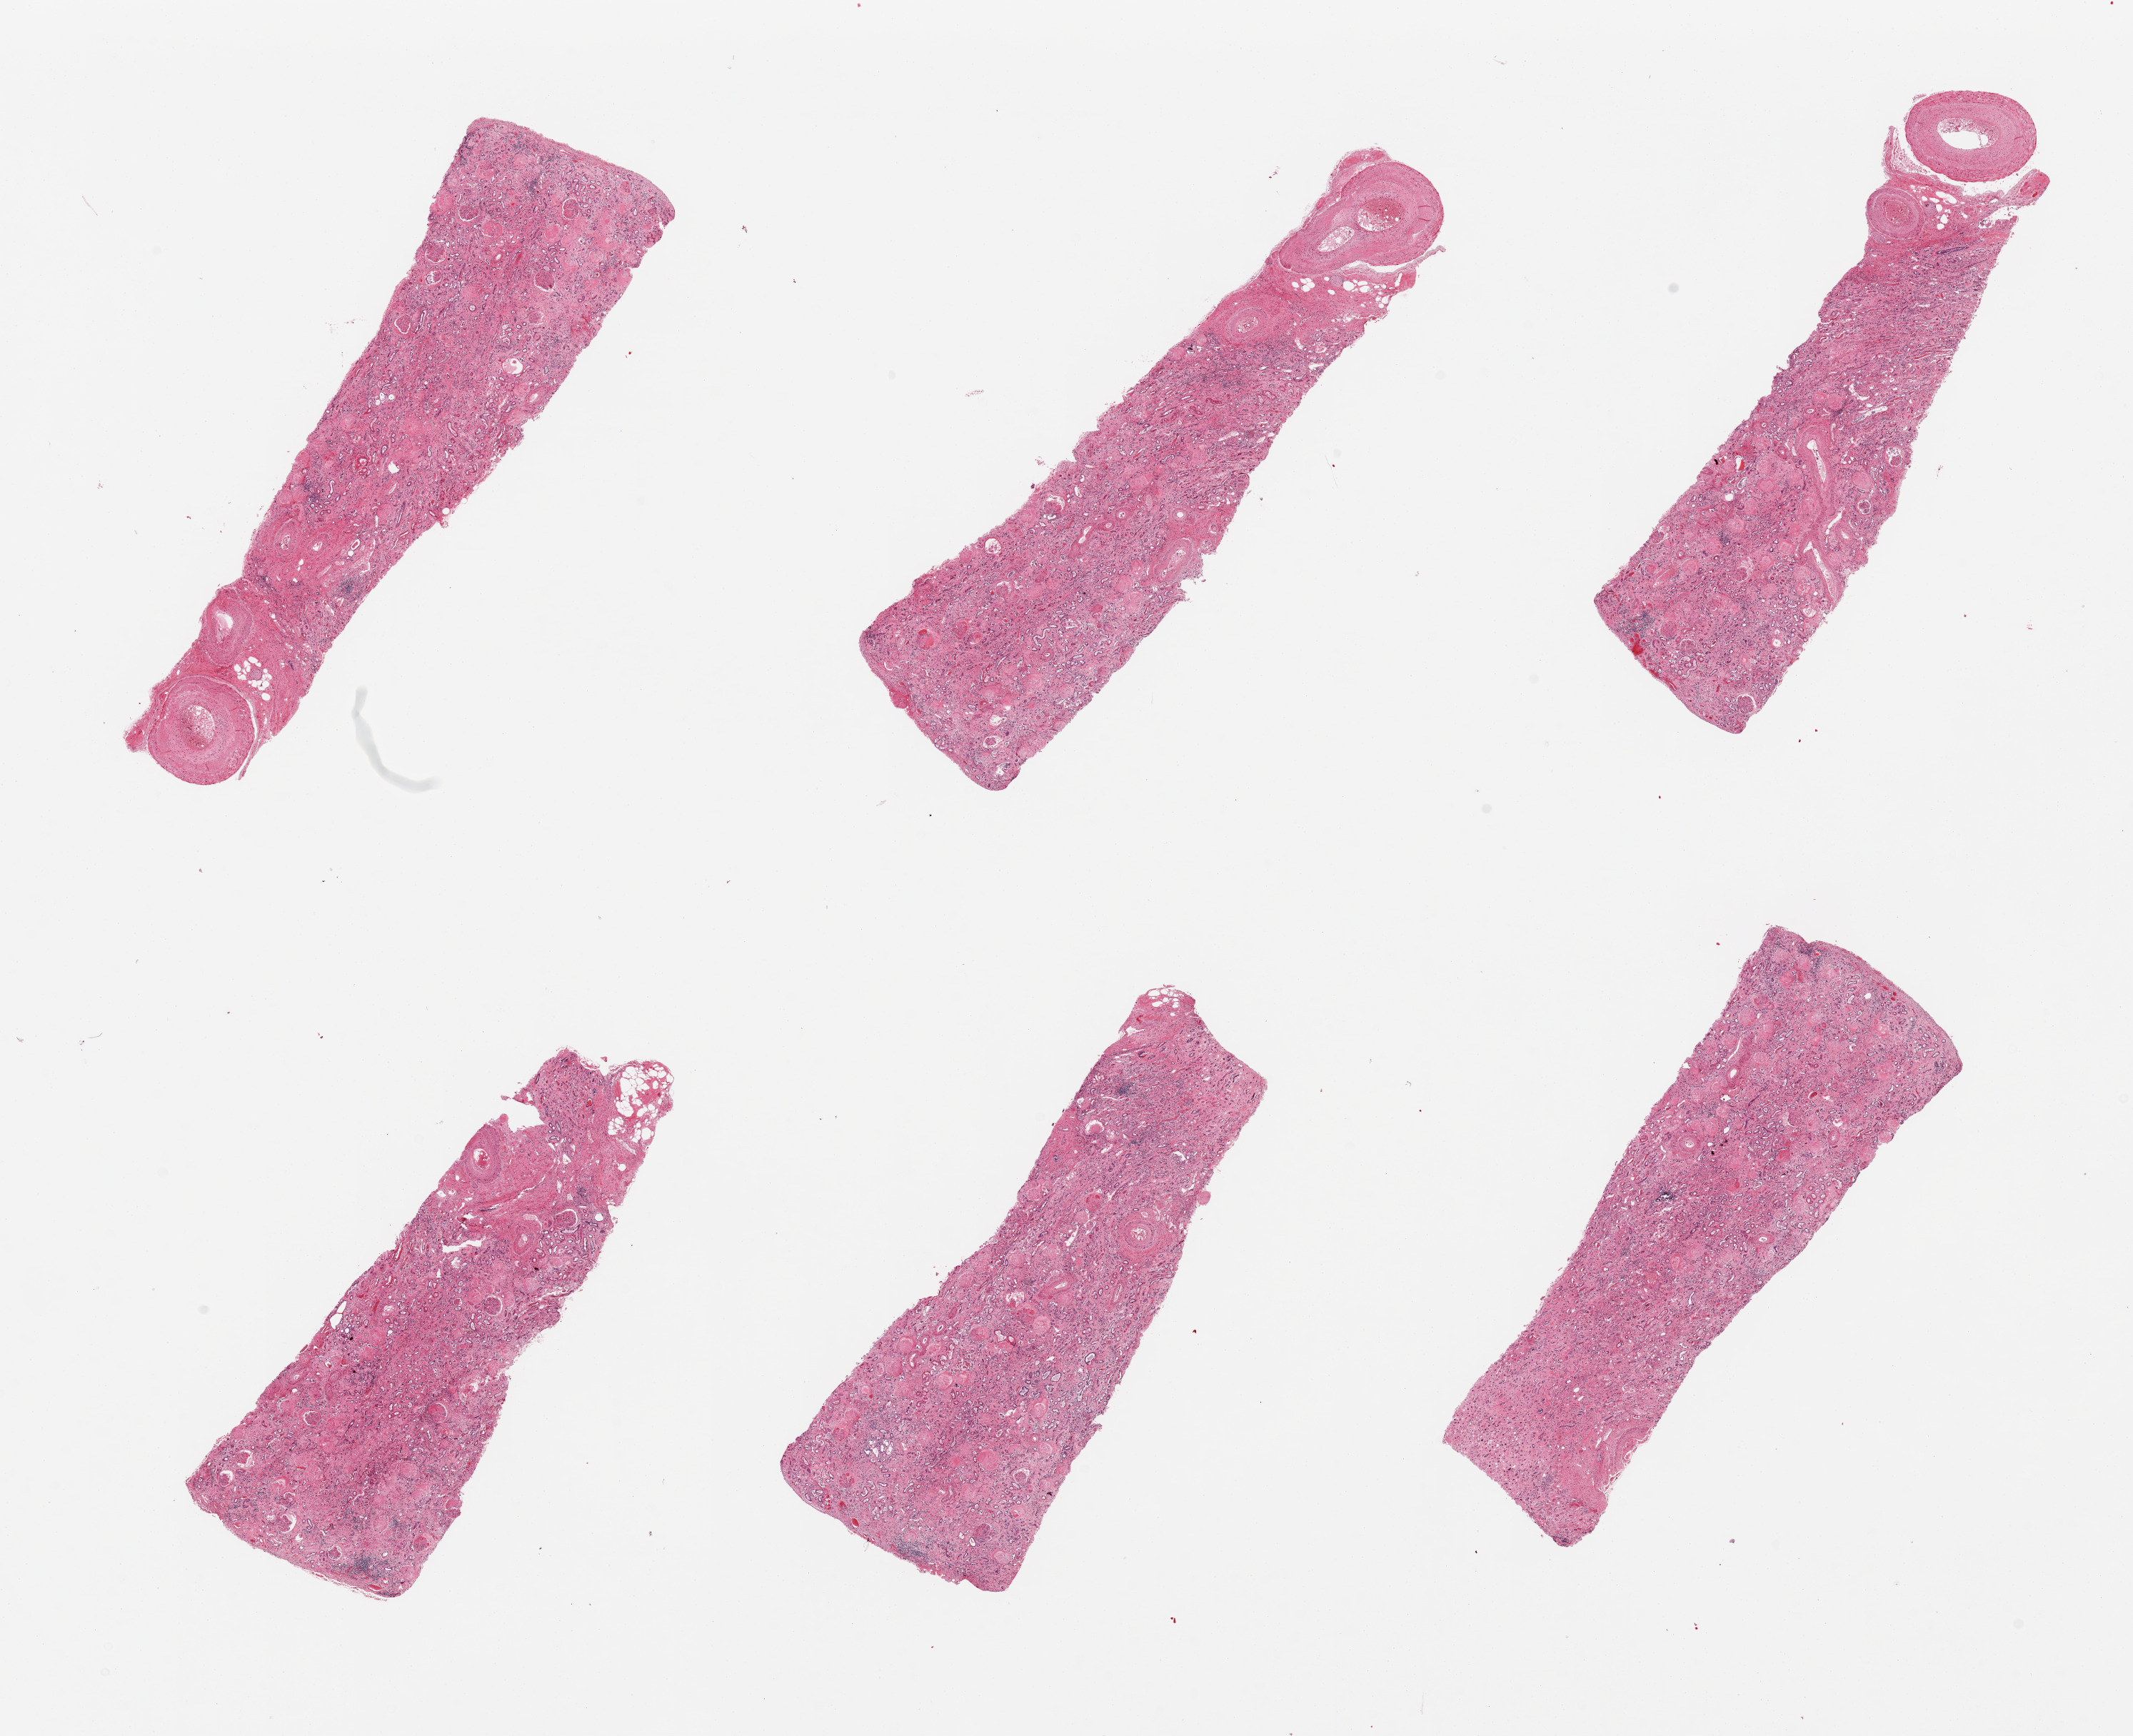
Whole-slide image, hematoxylin and eosin (H&E) stain, shown as a low-resolution overview of the whole scanned area (about 23.6 x 19.2 mm), PAXgene-fixed, paraffin-embedded tissue, target tissue: renal cortex, tissue donor sample. Male donor.
- review note (as recorded): 6 pieces, pronounced glomerulosclerosis/chronic interstitial nephritis, fibrosis